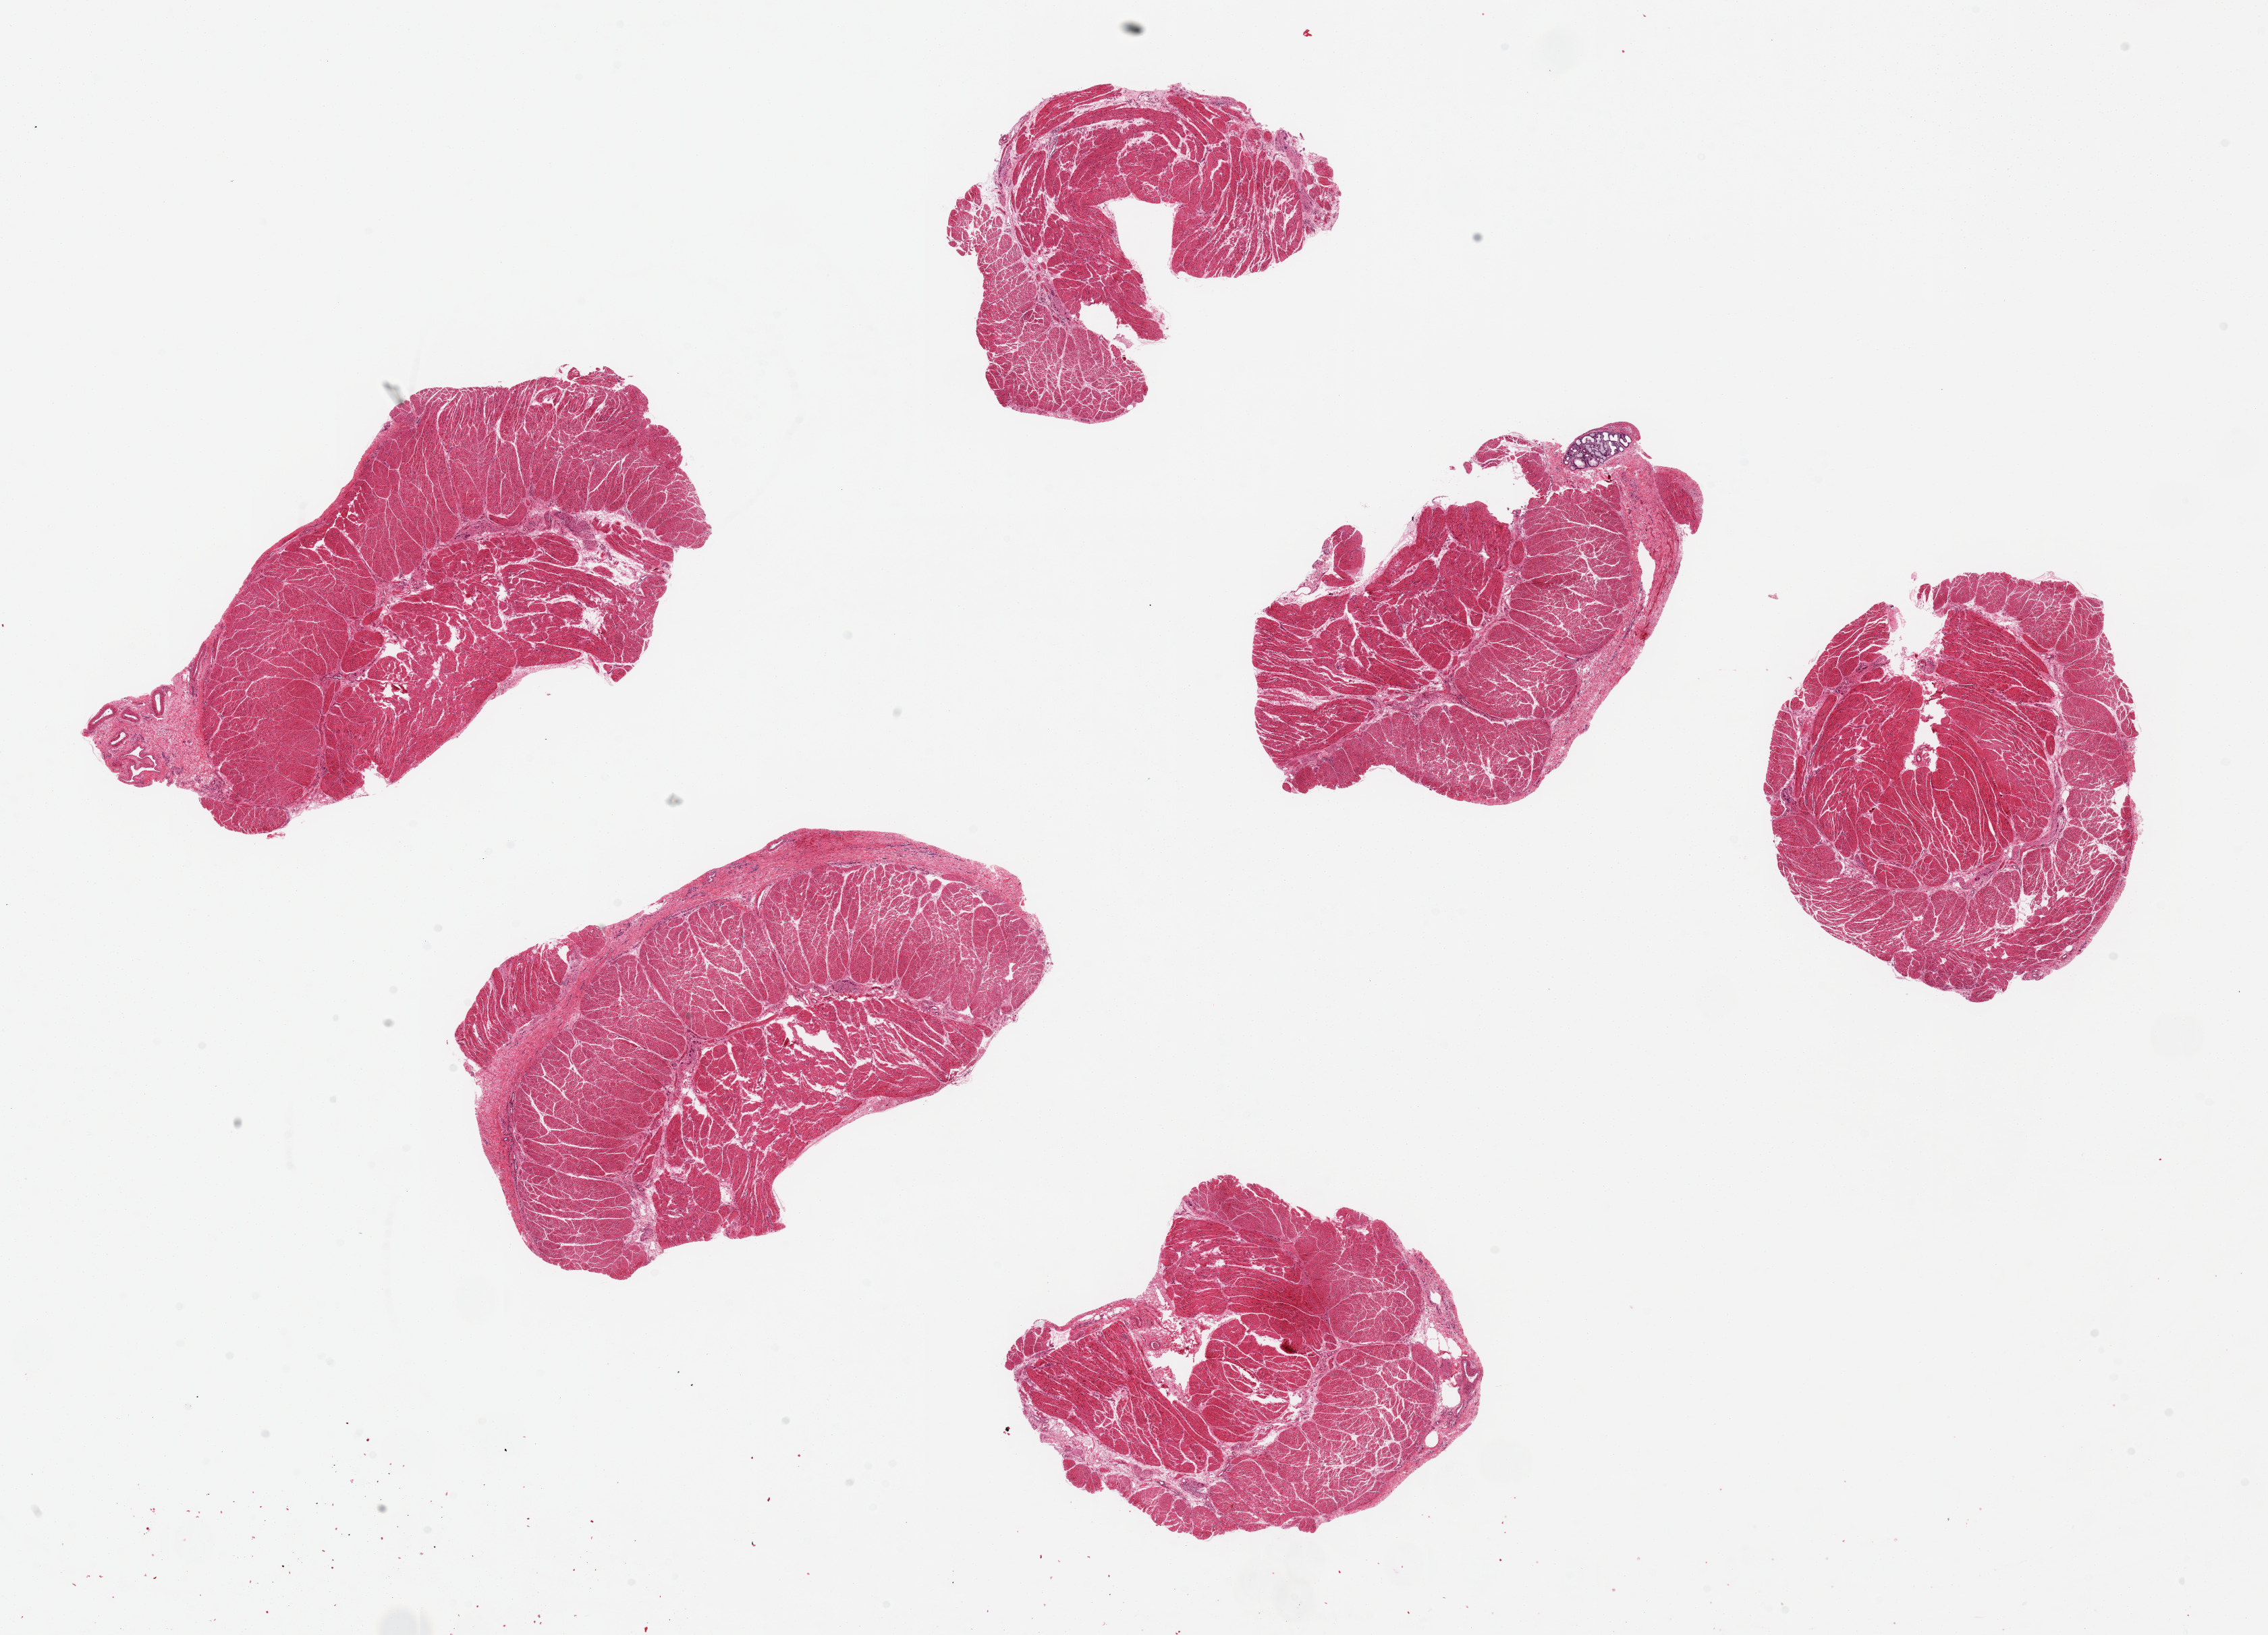
Whole-slide image, hematoxylin and eosin (H&E) stain, a low-resolution overview of the entire scanned area, about 26.6 x 19.2 mm (acquisition: 20x scan); PAXgene-fixed paraffin-embedded (PFPE) section; sampled site (target tissue): esophageal muscle; tissue donor sample. Female donor.
Review note (as recorded): 6 ~7x3.5mm pieces. Single 0.6mm focus of sub mucosa mucous/serous glands noted in one piece.